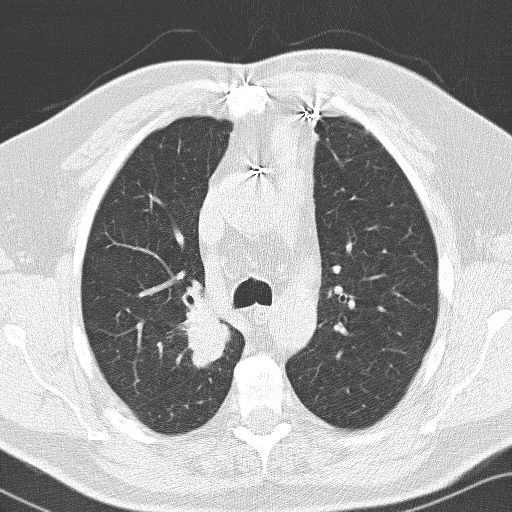
Axial slice from a low-dose chest CT screening exam. First (baseline) screen. Lung window (W 1500 / L -600 HU). 3.2 mm slice thickness. 120 kVp. Slice 39 of 141 in the series. 512 × 512 image matrix. Male participant, aged 66 years at enrolment. Former smoker at enrolment.
• Expert reader's lesion annotation, bounding box [x1, y1, x2, y2] px = [147, 296, 232, 390].
• Screening reader's record for this exam (one nodule recorded; not confirmed to be the boxed lesion): non-calcified nodule or mass ≥4 mm, right upper lobe, 36 × 30 mm, spiculated (stellate) margins, soft tissue attenuation.
• Official screen result: positive, change unspecified: nodule(s) >= 4 mm or enlarging nodule(s), mass(es), or other non-specific abnormalities suspicious for lung cancer.
• Participant outcome: lung cancer diagnosed 103 days after this screen — adenocarcinoma, NOS, right upper lobe, poorly differentiated (G3), stage IIB (AJCC 6th edition), 33 mm at pathology.